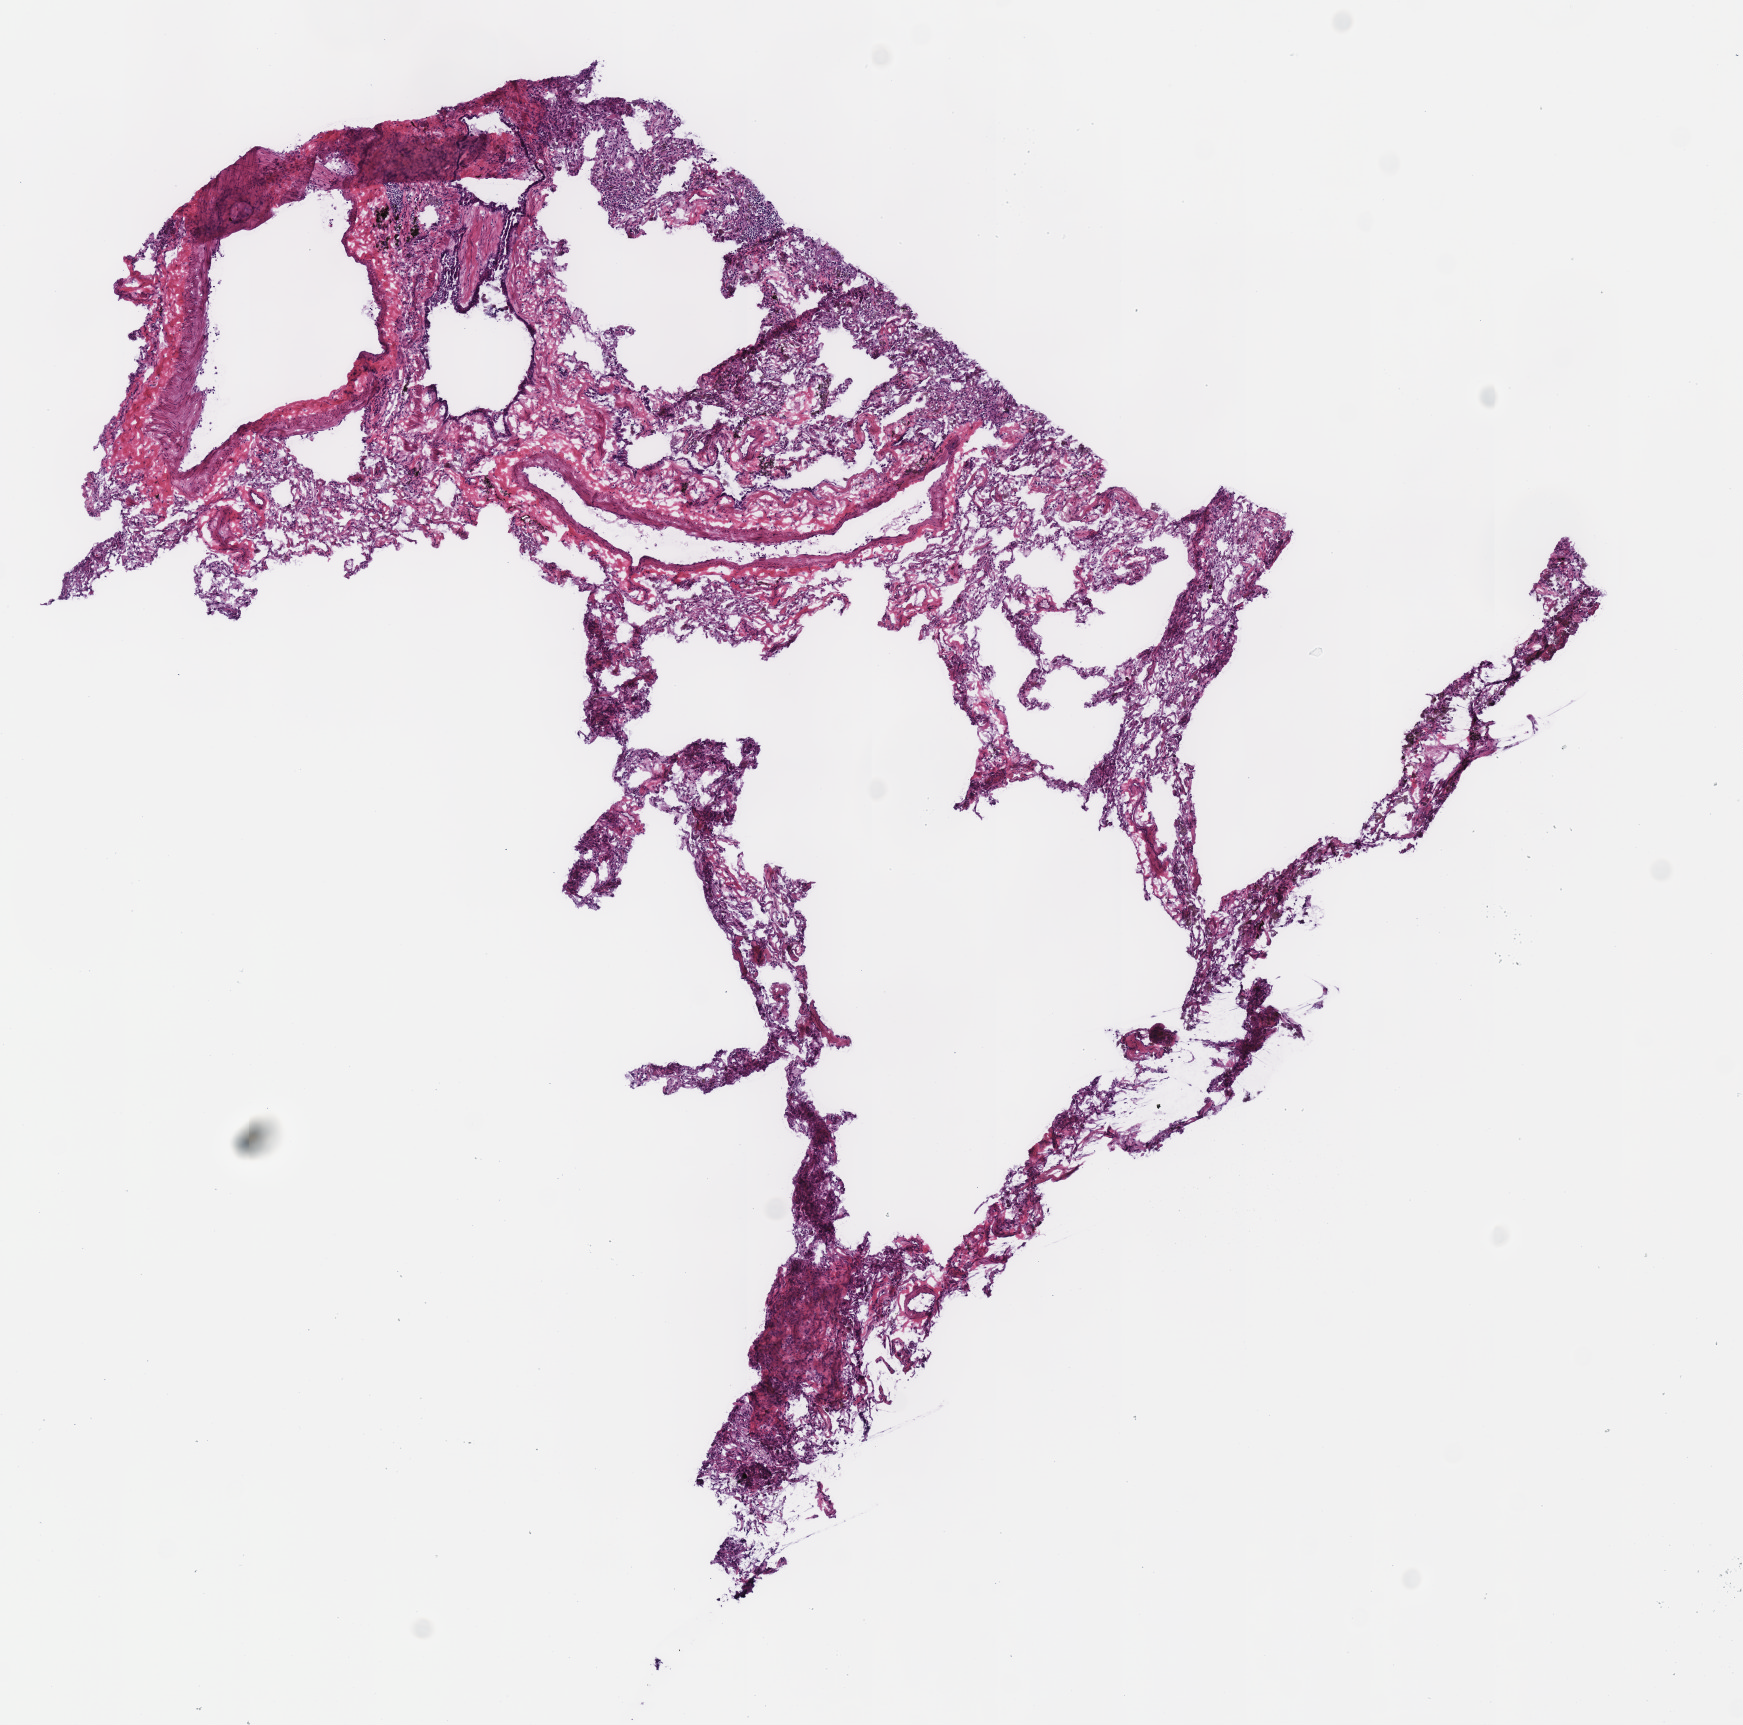
Digitized H&E tissue section (whole slide) — a low-resolution overview of the entire scanned area, about 6.9 x 6.8 mm (slide scanned at 40x); frozen section from the top of the tissue portion; solid tissue normal (non-tumour tissue) sample from the lung. Female patient; age at initial diagnosis 60 years.
This section: solid tissue normal sample (biorepository sample class). Patient diagnosis: Mucinous adenocarcinoma.